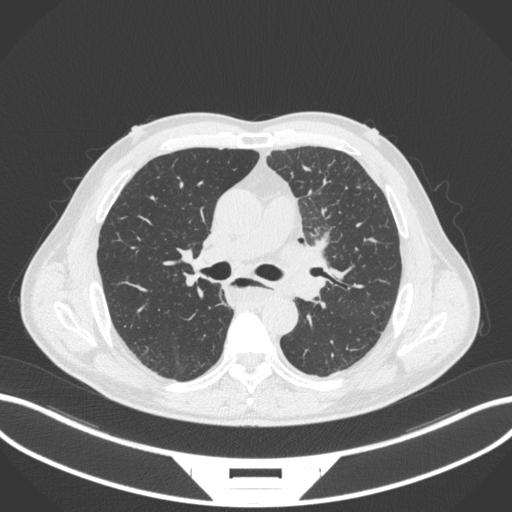
Chest CT, one axial slice. Slice 230 of 411 in the series (ordered by position). Reconstruction kernel B31f. 120 kVp. Lung window (W 1500 / L -600 HU). 1 mm slice thickness. 512 × 512 image matrix, field of view 400 × 400 mm. Patient: male, 57 years. Case-level facts recorded for this patient, not image findings: clinical TNM (as recorded): T2a N1 M0.
Outlined on this slice (bounding box drawn by a radiologist):
- lung tumour (recorded histology: squamous cell carcinoma): box from (x=281, y=234) to (x=340, y=275) px